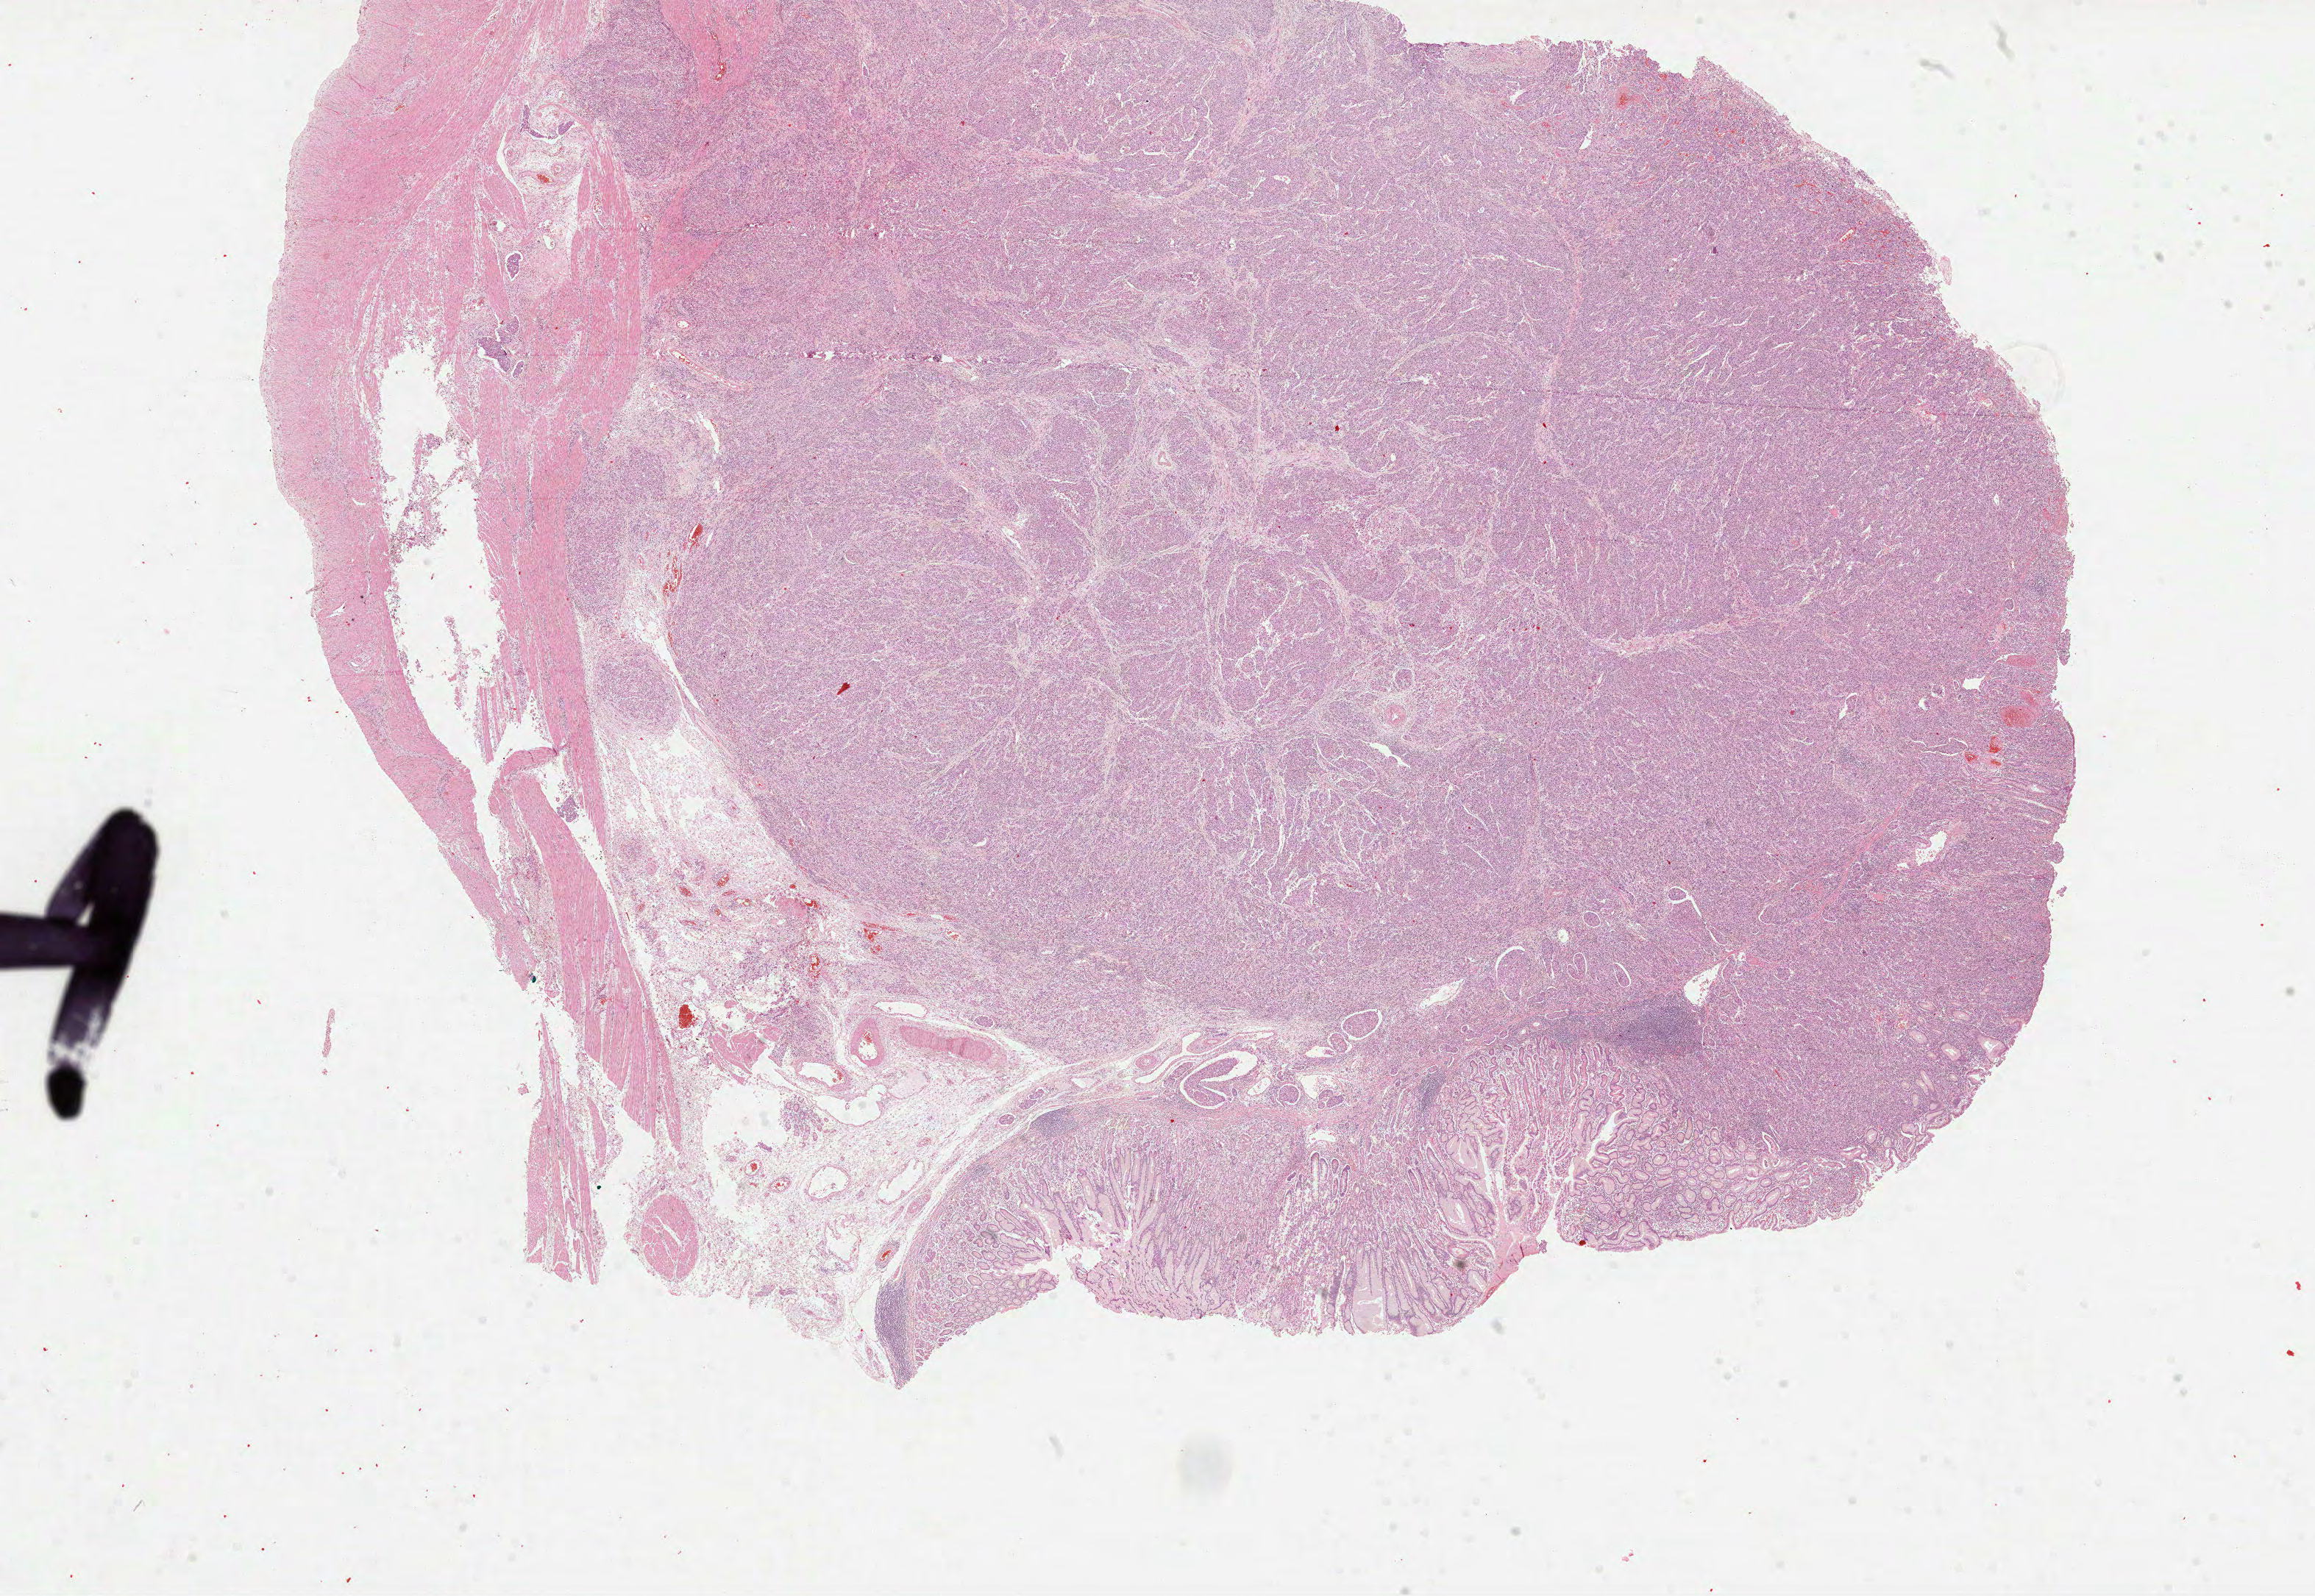
H&E-stained whole-slide image — a low-resolution overview of the entire scanned area, about 25.4 x 17.5 mm (slide scanned at 40x), formalin-fixed paraffin-embedded (FFPE) diagnostic section, primary tumour sample from the stomach. Male, age 53 years at initial diagnosis. Histologic grade: G3 (poorly differentiated).
* diagnosis: Tubular adenocarcinoma (gastric antrum)
* lymph nodes positive (case pathology): 14 of 24 examined
* TNM: T2b N2 M0
* AJCC pathologic stage: IIIA